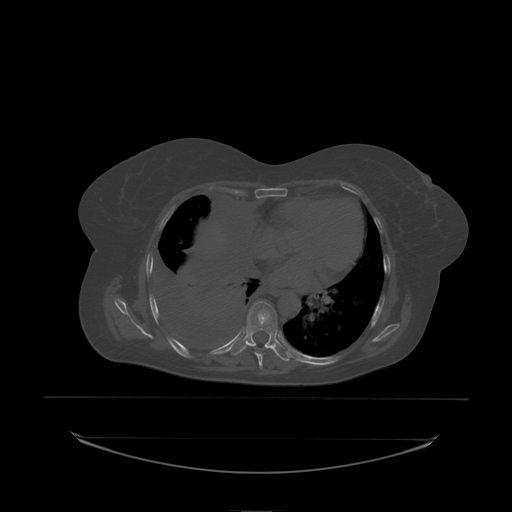
CT including the spine, one axial slice; position 136 of 242 along the scan axis; bone window (W 1800 / L 400 HU); 512 × 512 image matrix, field of view 500 × 500 mm. Patient: female, 53 years. From the clinical record (not read from this slice): primary cancer: lung.
Annotated regions visible in this slice (semi-automatically segmented with operator editing):
- T8 vertebra: bounding box [x1, y1, x2, y2] px = [246, 301, 278, 338]